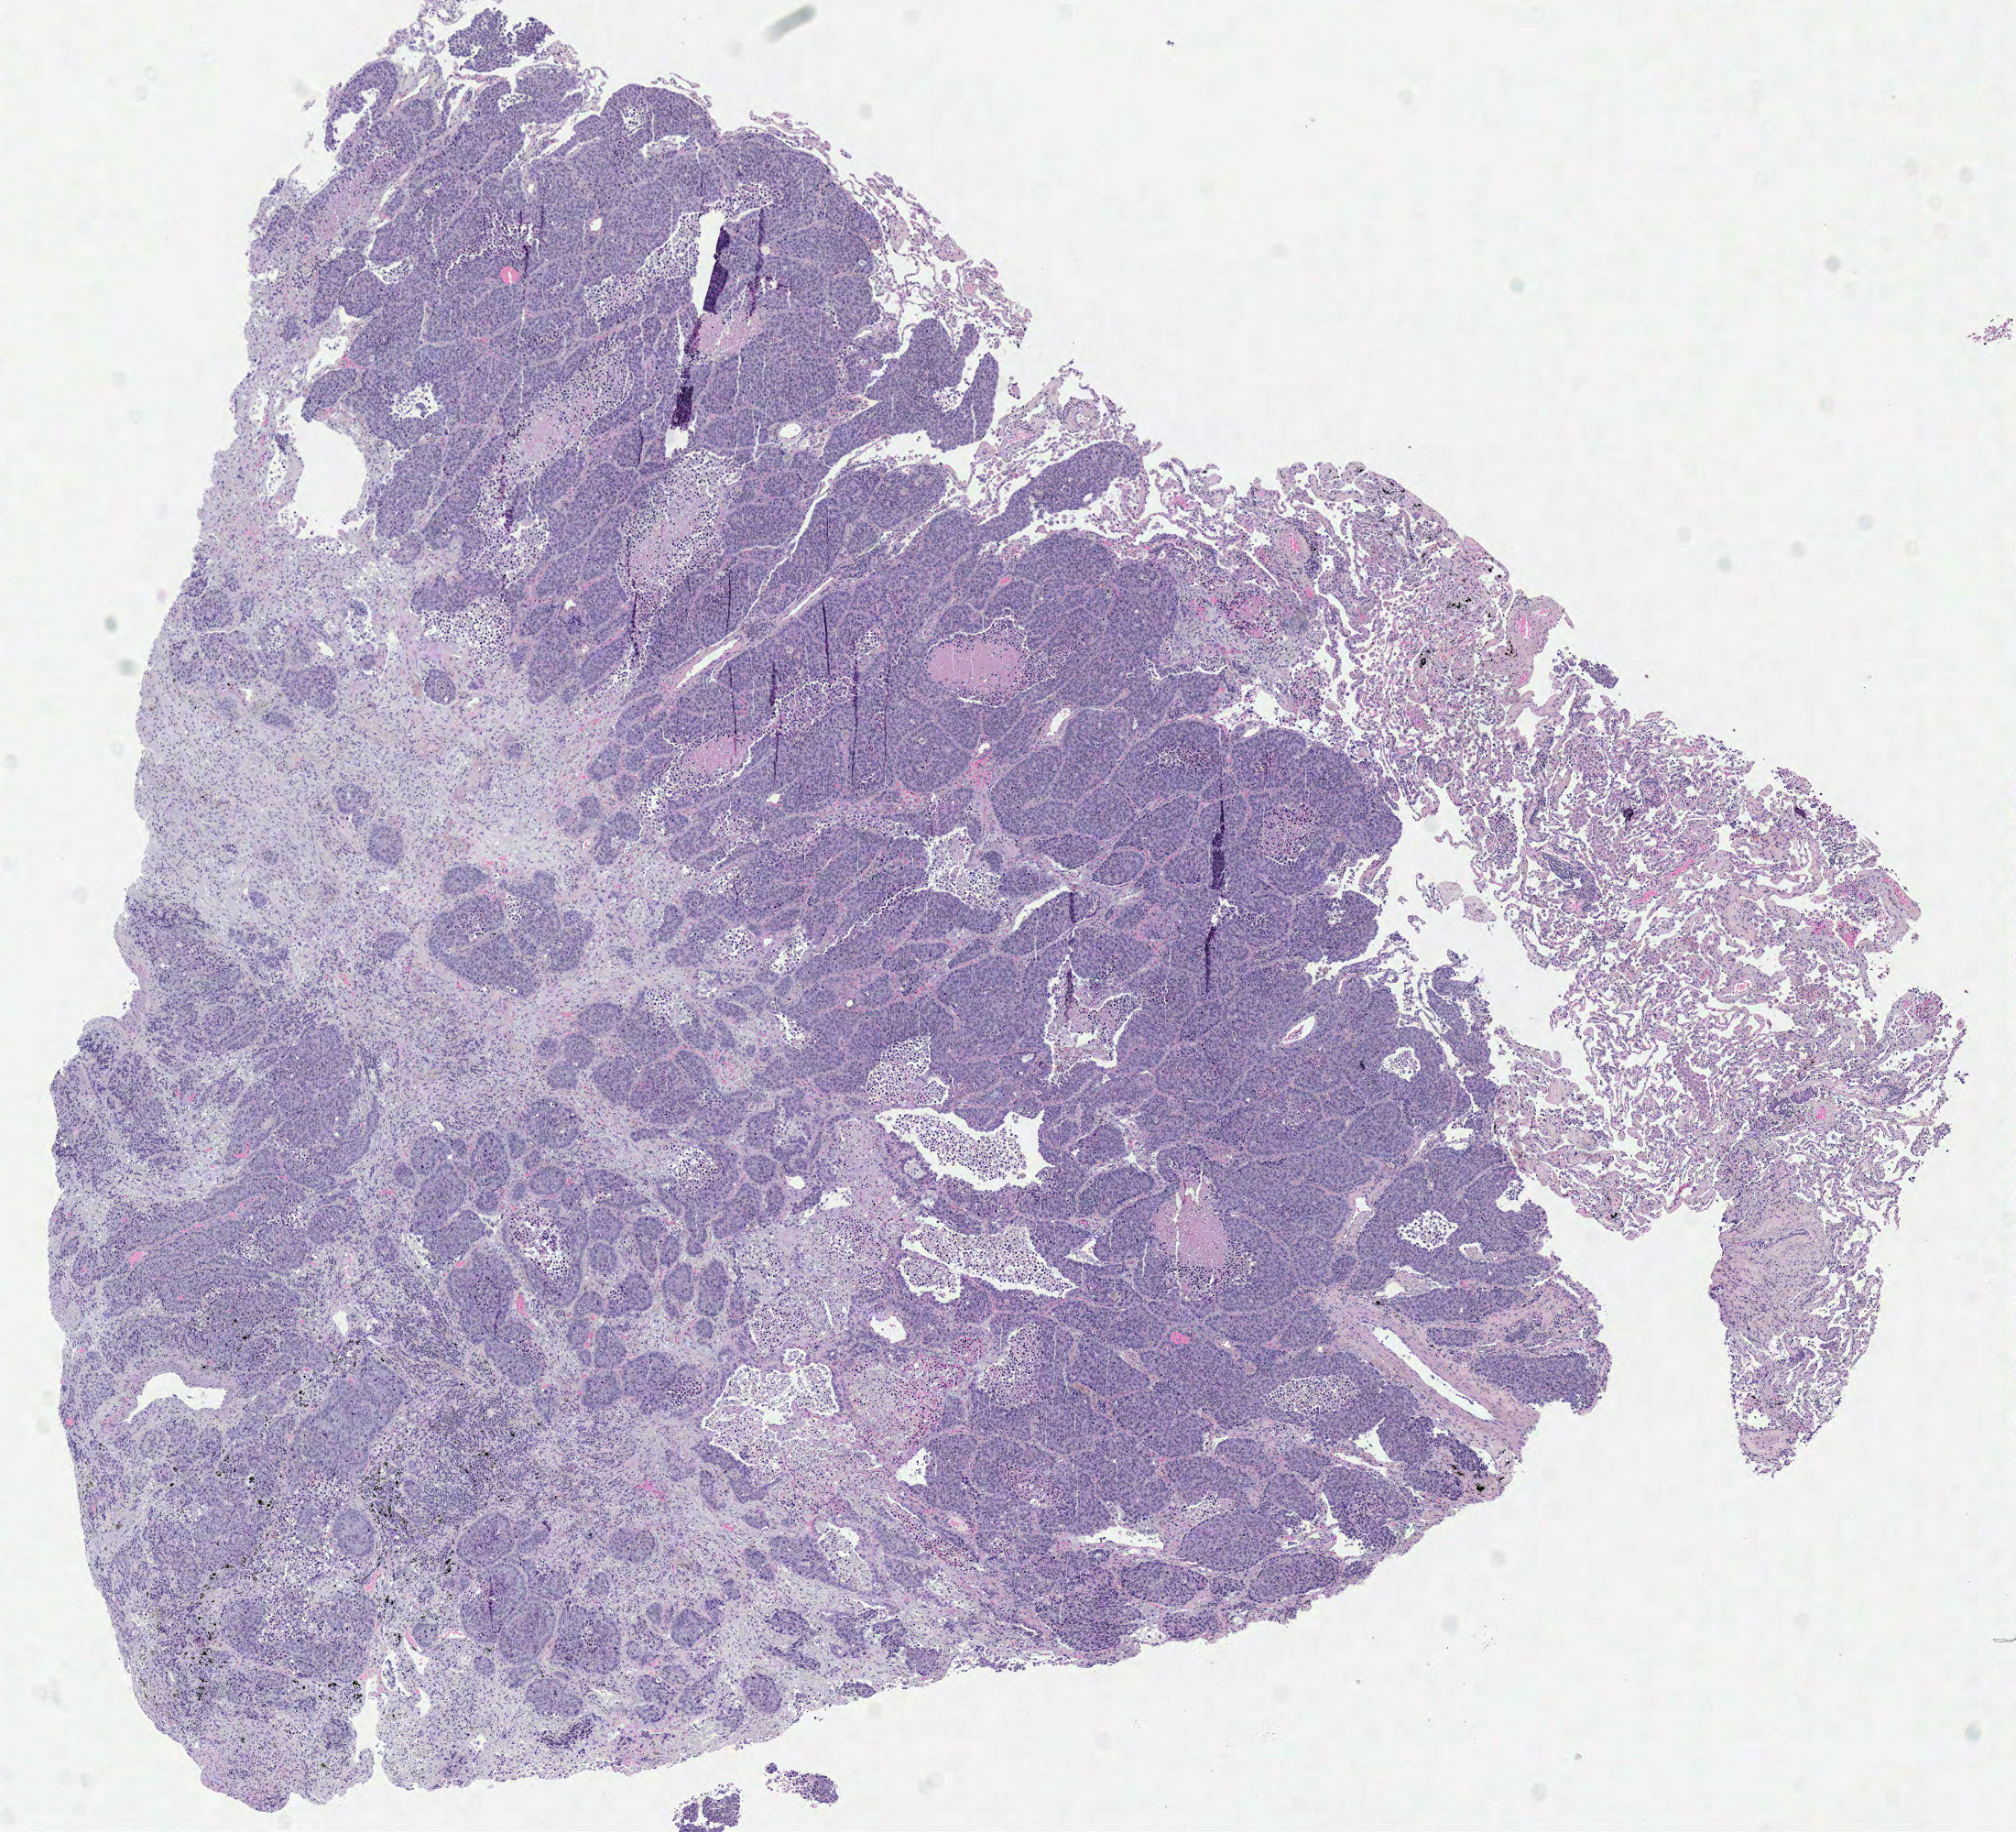
Digitized H&E-stained tissue section (whole slide) — whole scanned area (about 8.7 x 7.9 mm) shown as a low-resolution overview, formalin-fixed paraffin-embedded (FFPE) diagnostic section, lung, primary tumour sample. Male, age 66 years at initial diagnosis.
• laterality: right
• histologic diagnosis: Squamous cell carcinoma, NOS (upper lobe, lung)
• AJCC pathologic stage: IIIA